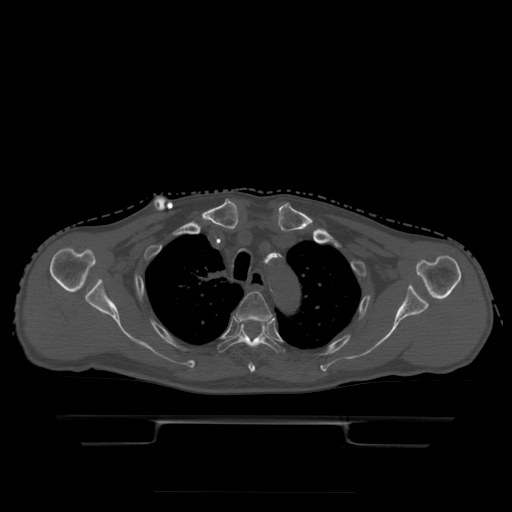
CT including the spine, one axial slice; slice 362 of 522 in the series (ordered by position); bone window (W 1800 / L 400 HU); 1.25 mm slice thickness; 512 × 512 image matrix, field of view 436 × 436 mm. Patient age 68 years. From the clinical record (not read from this slice): primary cancer: urothelial.
Structures marked on this image (semi-automatic segmentation, software-assisted and operator-edited):
- T3 vertebra: bounding box [x1, y1, x2, y2] px = [237, 292, 273, 373]
- T4 vertebra: [217, 320, 286, 354]